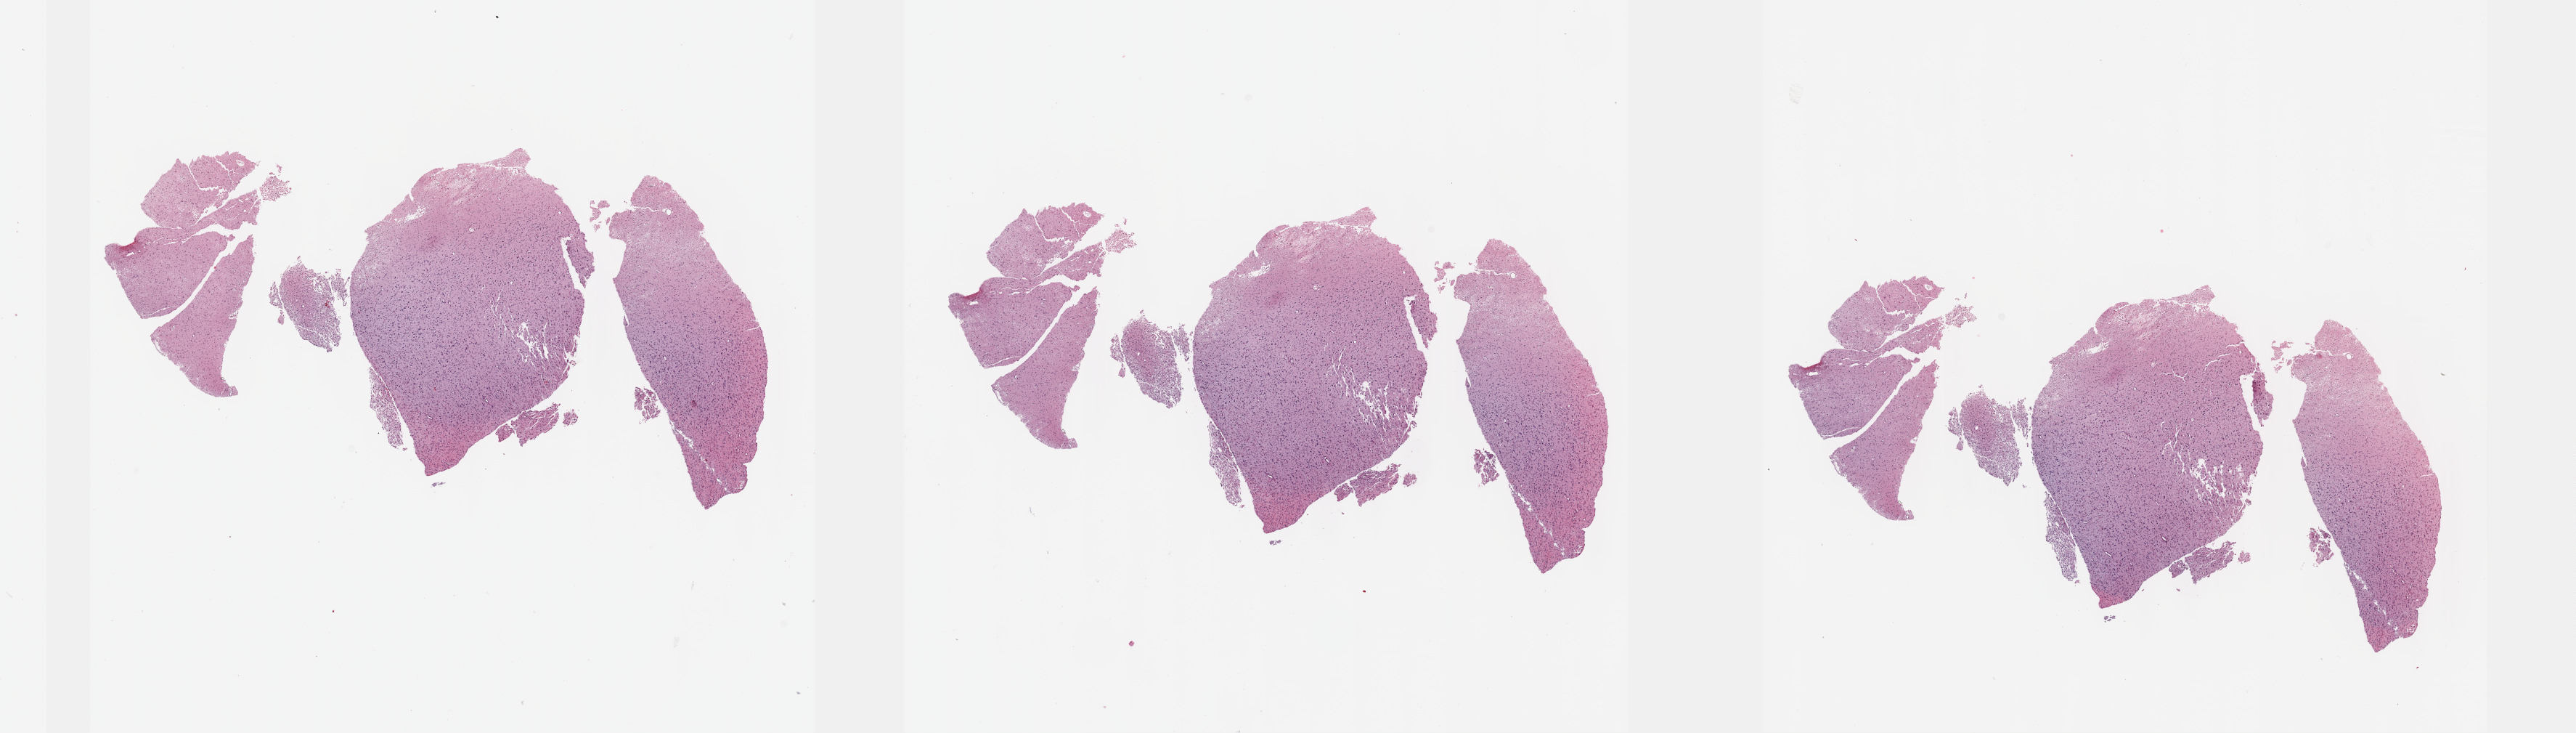
Whole-slide histology image, Hematoxylin and eosin (H&E) stained, a low-resolution overview of the entire scanned area, about 28.7 x 8.2 mm (from a 40x scan), formalin-fixed paraffin-embedded (FFPE) diagnostic section, sample: primary tumour, brain. Male patient; age at initial diagnosis 69 years. Histologic grade: G3 (poorly differentiated).
• diagnosis: Astrocytoma, anaplastic (cerebrum)
• laterality: left